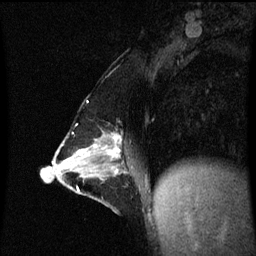
Breast MRI (dynamic contrast-enhanced), one sagittal slice. Position 27 of 60 along the scan axis. Dynamic contrast-enhanced series, image 2 of 3 at this slice position (ordered by acquisition). 1.5 T. TE 4.2 ms, TR 8.9 ms. 256 × 256 image matrix, field of view 200 × 200 mm. Patient: female, 47 years. From the clinical record (not read from this slice): setting: breast cancer imaged before/during neoadjuvant chemotherapy; receptor status: HR-positive, HER2-negative.
Annotated regions visible in this slice (semi-automatic segmentation, software-assisted and operator-edited):
- analysis volume of interest (the breast-tissue region the enhancement analysis was run in; not a lesion): box from (x=53, y=134) to (x=129, y=209) px
- tumour enhancement mask (voxels above the 70 % enhancement threshold inside the analysis volume of interest): (x=55, y=134)–(x=122, y=175)